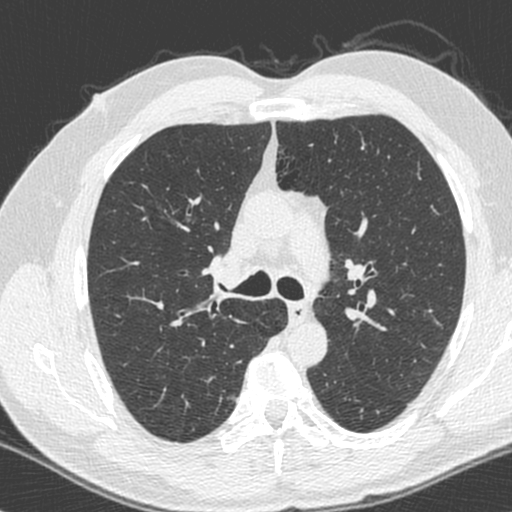
Chest CT (low-dose screening protocol), one axial image, first (baseline) screen, lung window (W 1500 / L -600 HU), standard (soft-tissue) reconstruction kernel (C), 512 × 512 image matrix. Male, age 55 years at enrolment.
Expert-annotated lung lesion, bounding box (x1, y1, x2, y2) in pixels: (216, 385, 246, 410). No non-calcified nodule or mass ≥4 mm was recorded by the screening reader at this exam. Official screen result: negative screen, minor abnormalities not suspicious for lung cancer.